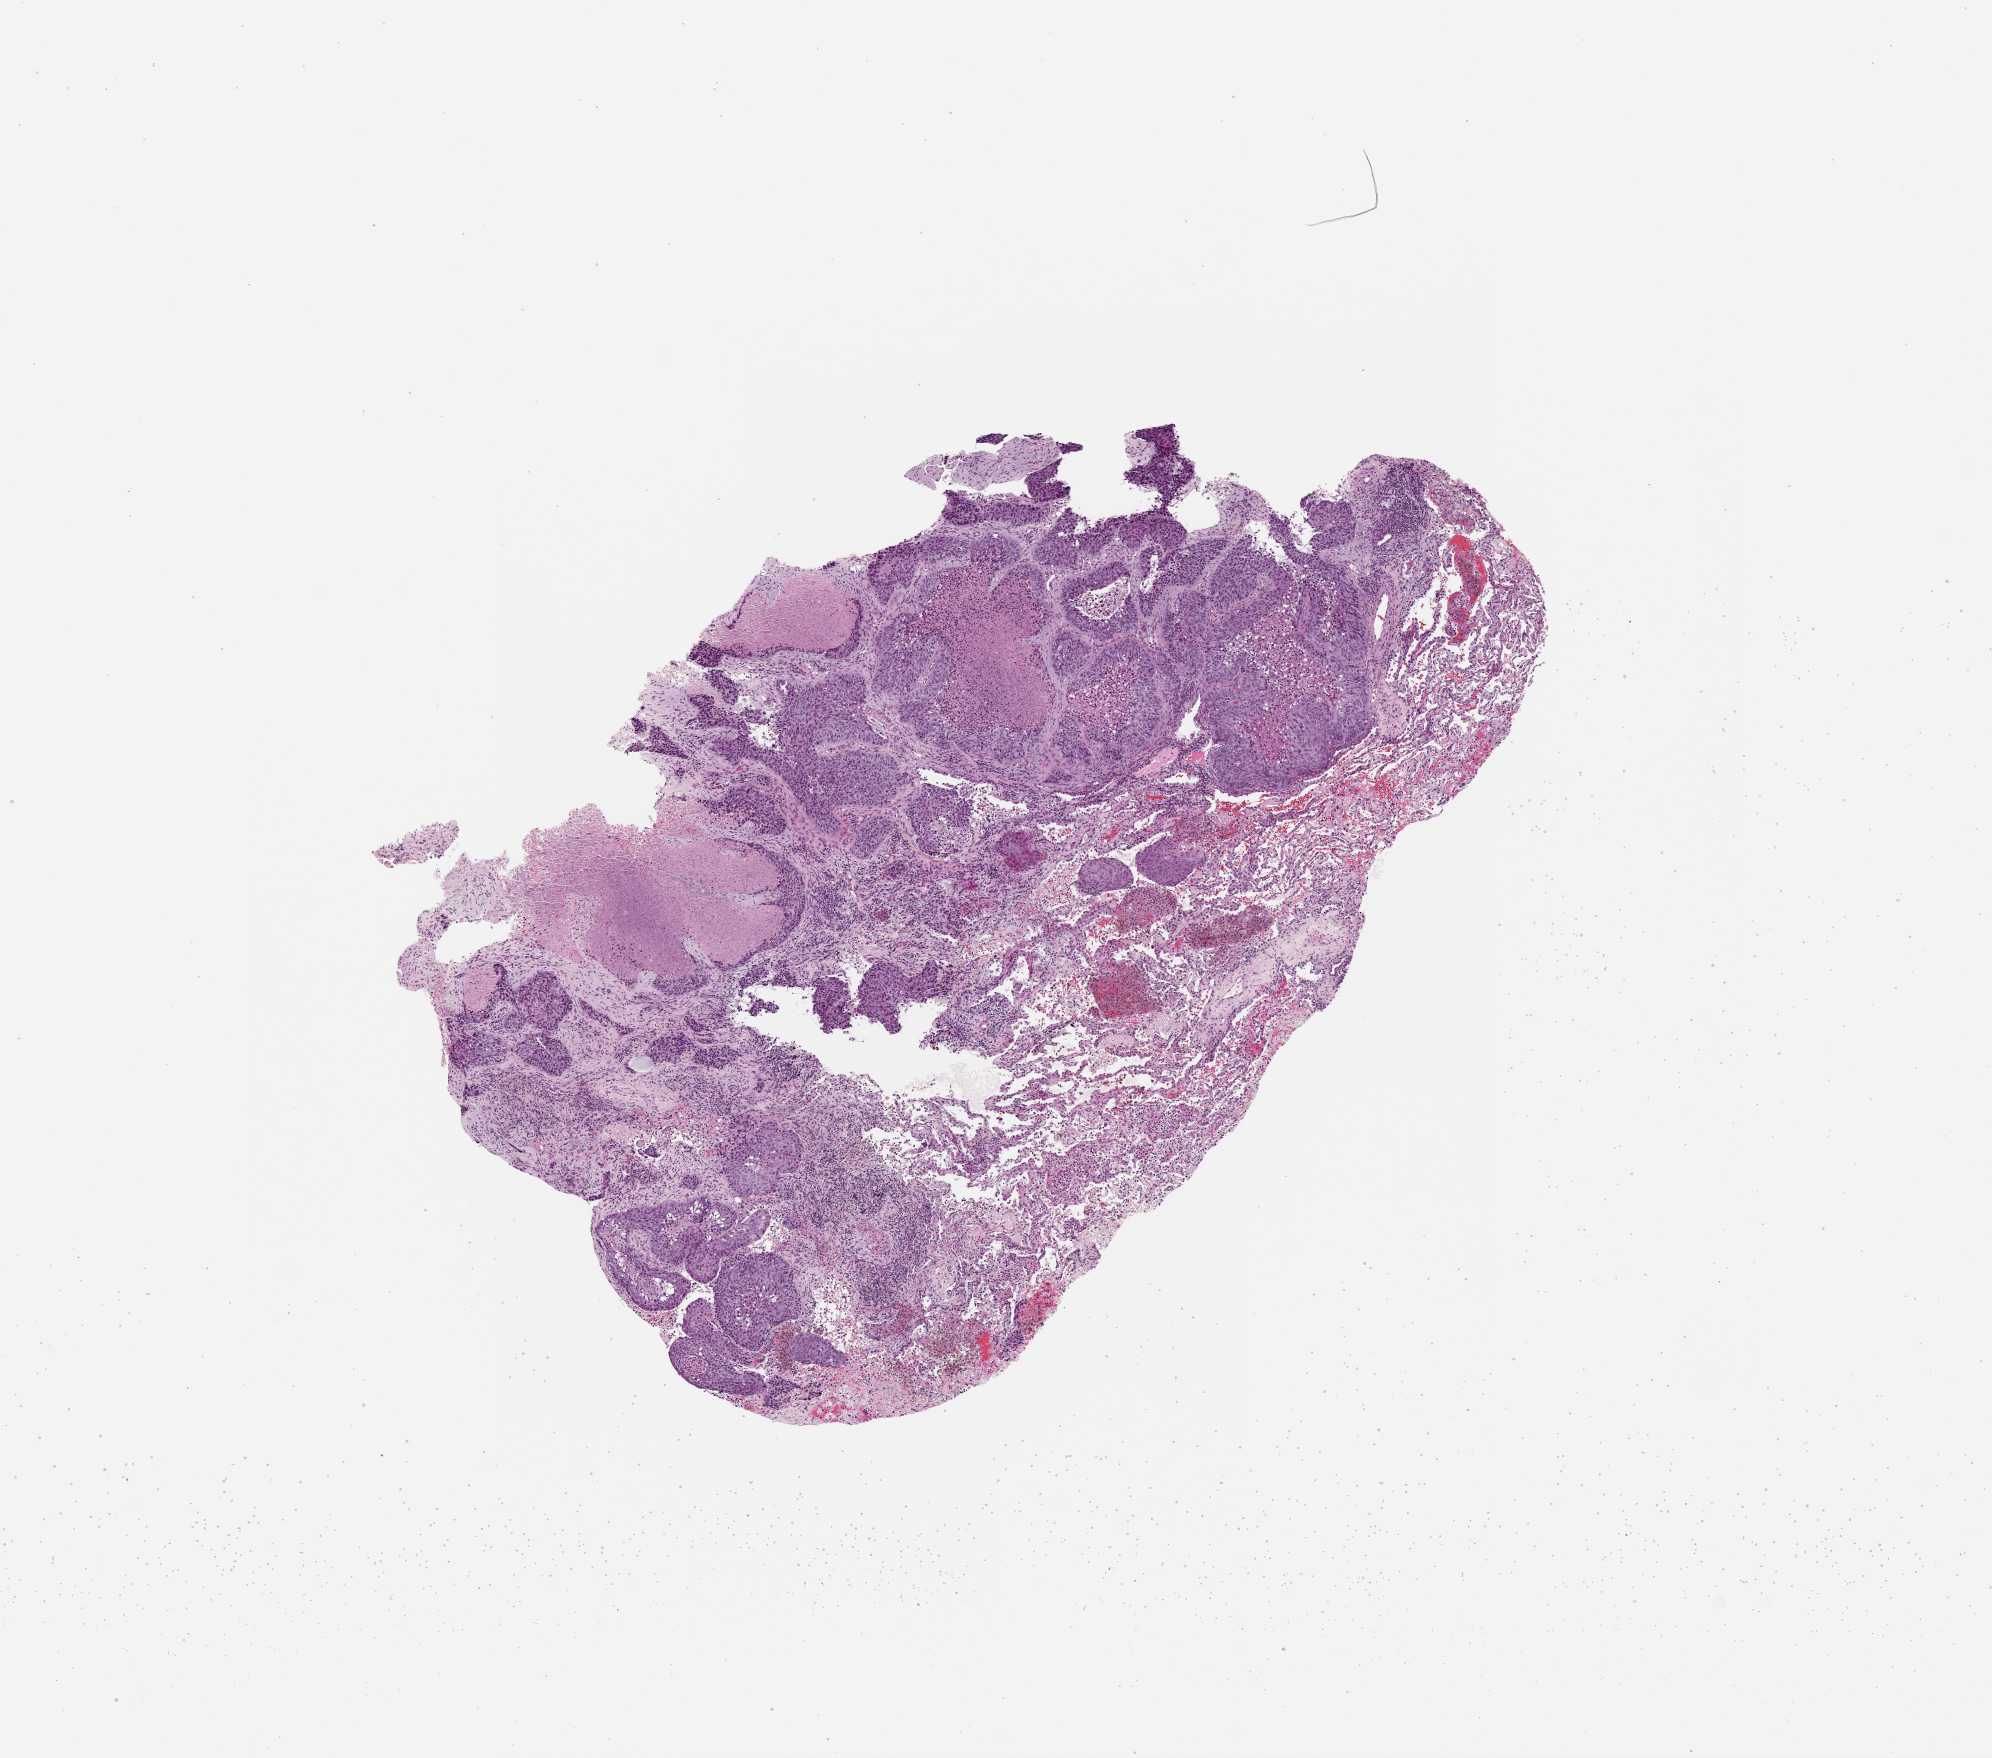
H&E-stained whole-slide image — low-resolution overview of the scanned area, about 8.0 x 7.1 mm (acquisition: 20x scan), tumour tissue sample, lung. Male, 62 y/o.
Patient diagnosis (cohort enrolment): squamous cell carcinoma (lung).